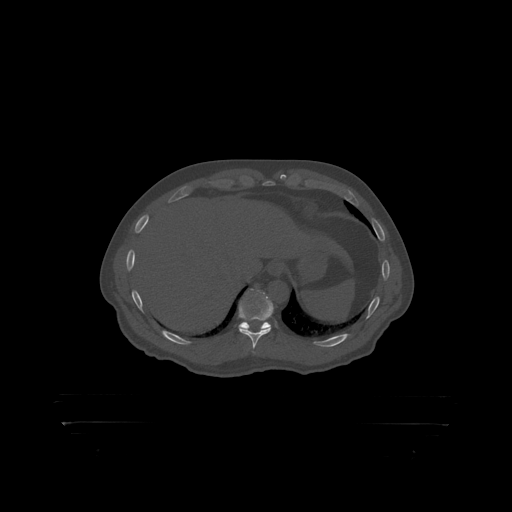
CT including the spine, one axial slice. Reconstruction kernel STANDARD. Bone window (W 1800 / L 400 HU). 1.25 mm slice thickness. 512 × 512 image matrix. Patient: male, 46 years. From the clinical record (not read from this slice): primary cancer: skin.
Structures marked on this image (semi-automatically segmented with operator editing):
- T10 vertebra: bounding box [x1, y1, x2, y2] px = [240, 292, 273, 319]